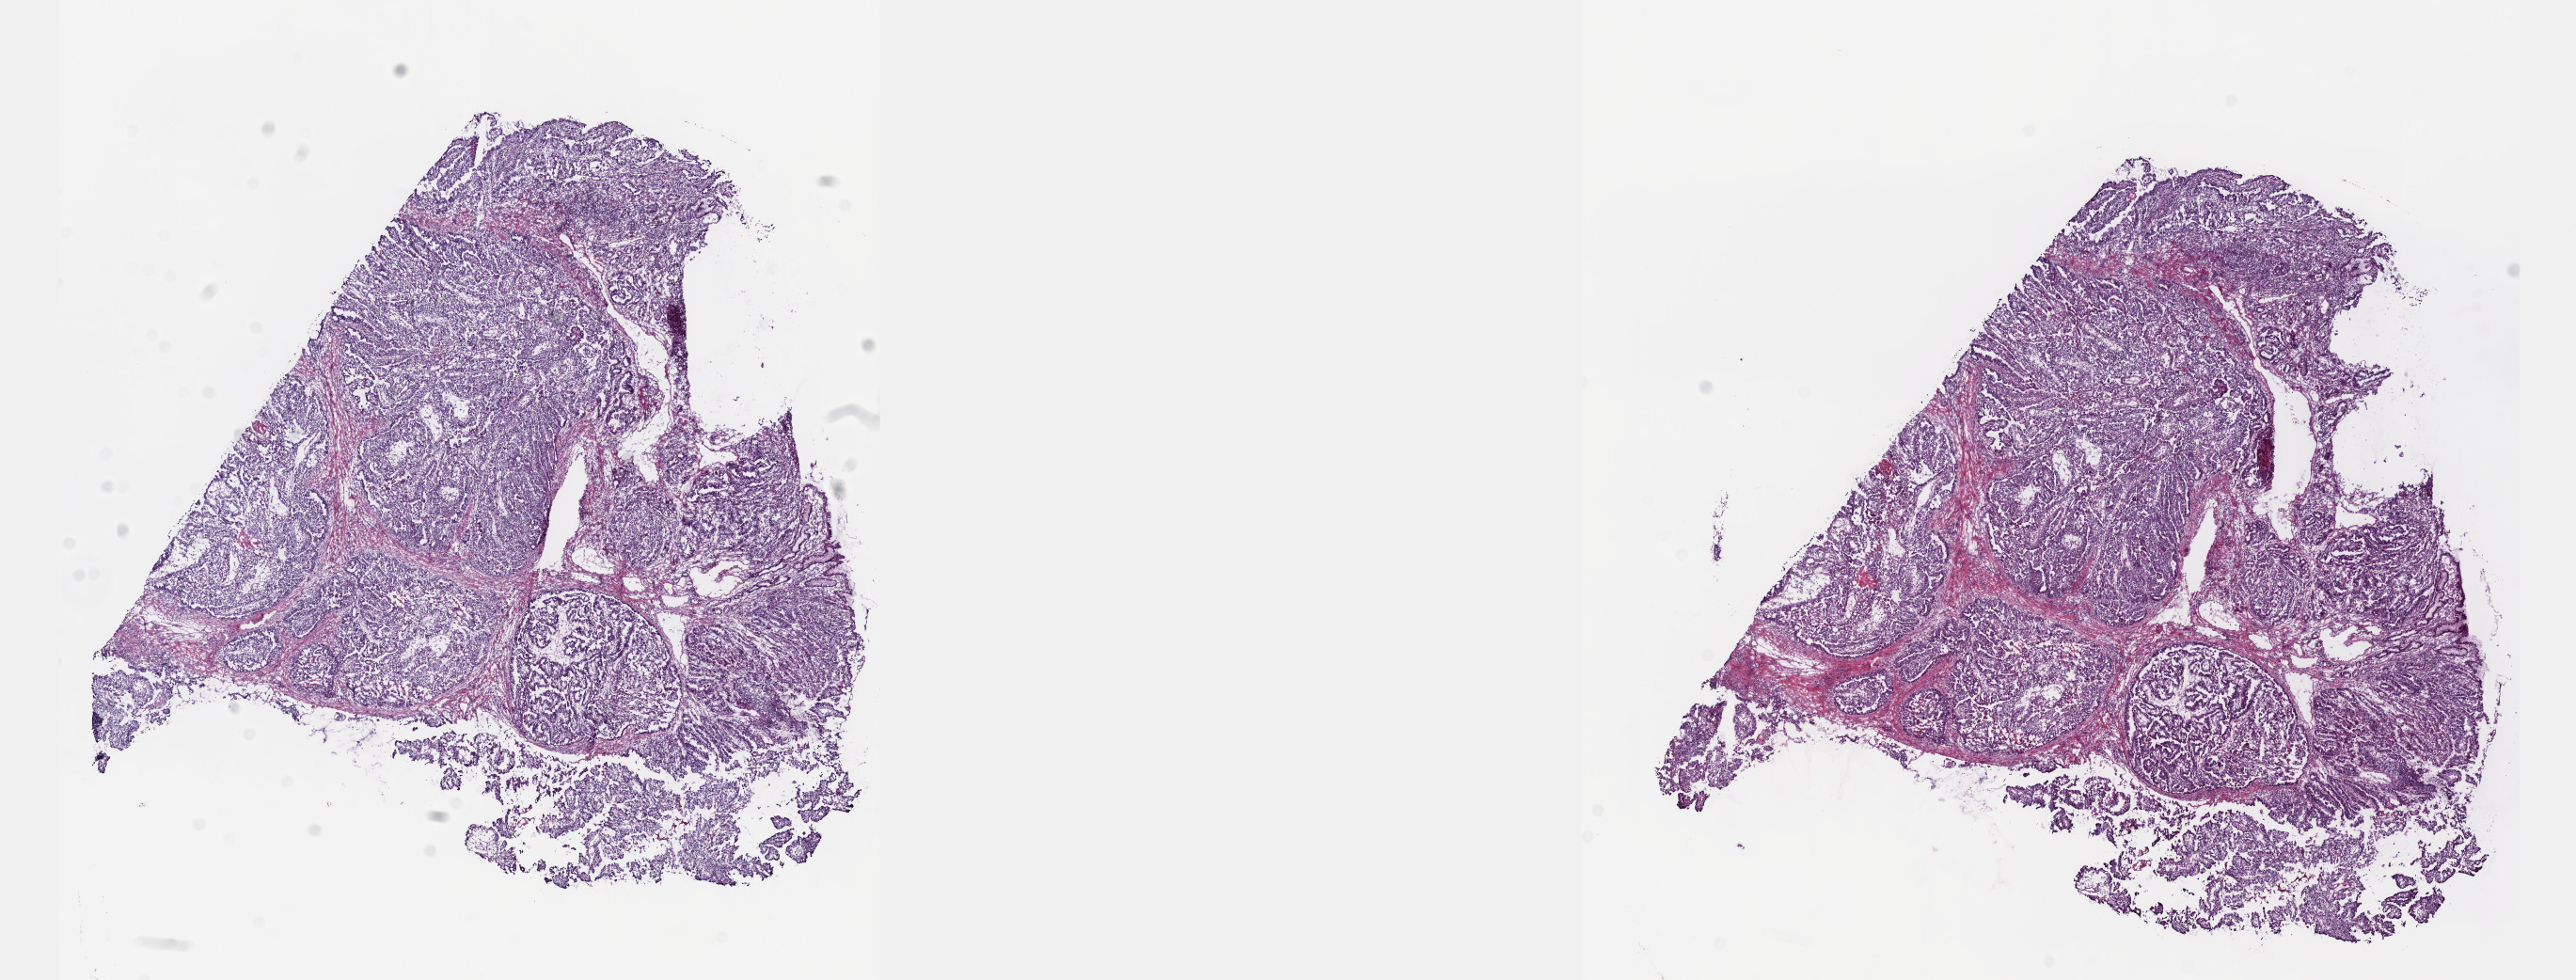
Digitized H&E-stained tissue section (whole slide), shown as a low-resolution overview of the whole scanned area (about 22.1 x 8.4 mm); frozen section from the top of the tissue portion; stomach, primary tumour sample. Patient: male, age at initial diagnosis 53 years. Histologic grade: GX (grade cannot be assessed). Slide review estimates, as recorded: tumour cells 85%, tumour nuclei 85%, normal cells 0%, stromal cells 15%, necrosis 0%. Inflammatory infiltration, as recorded: lymphocyte infiltration 3%, monocyte infiltration 1%, neutrophil infiltration 3%.
TNM: T4 N2 M1. AJCC pathologic stage: IV. Lymph nodes positive (case pathology): 9 of 24 examined. Pathologic diagnosis: Tubular adenocarcinoma (body of stomach).